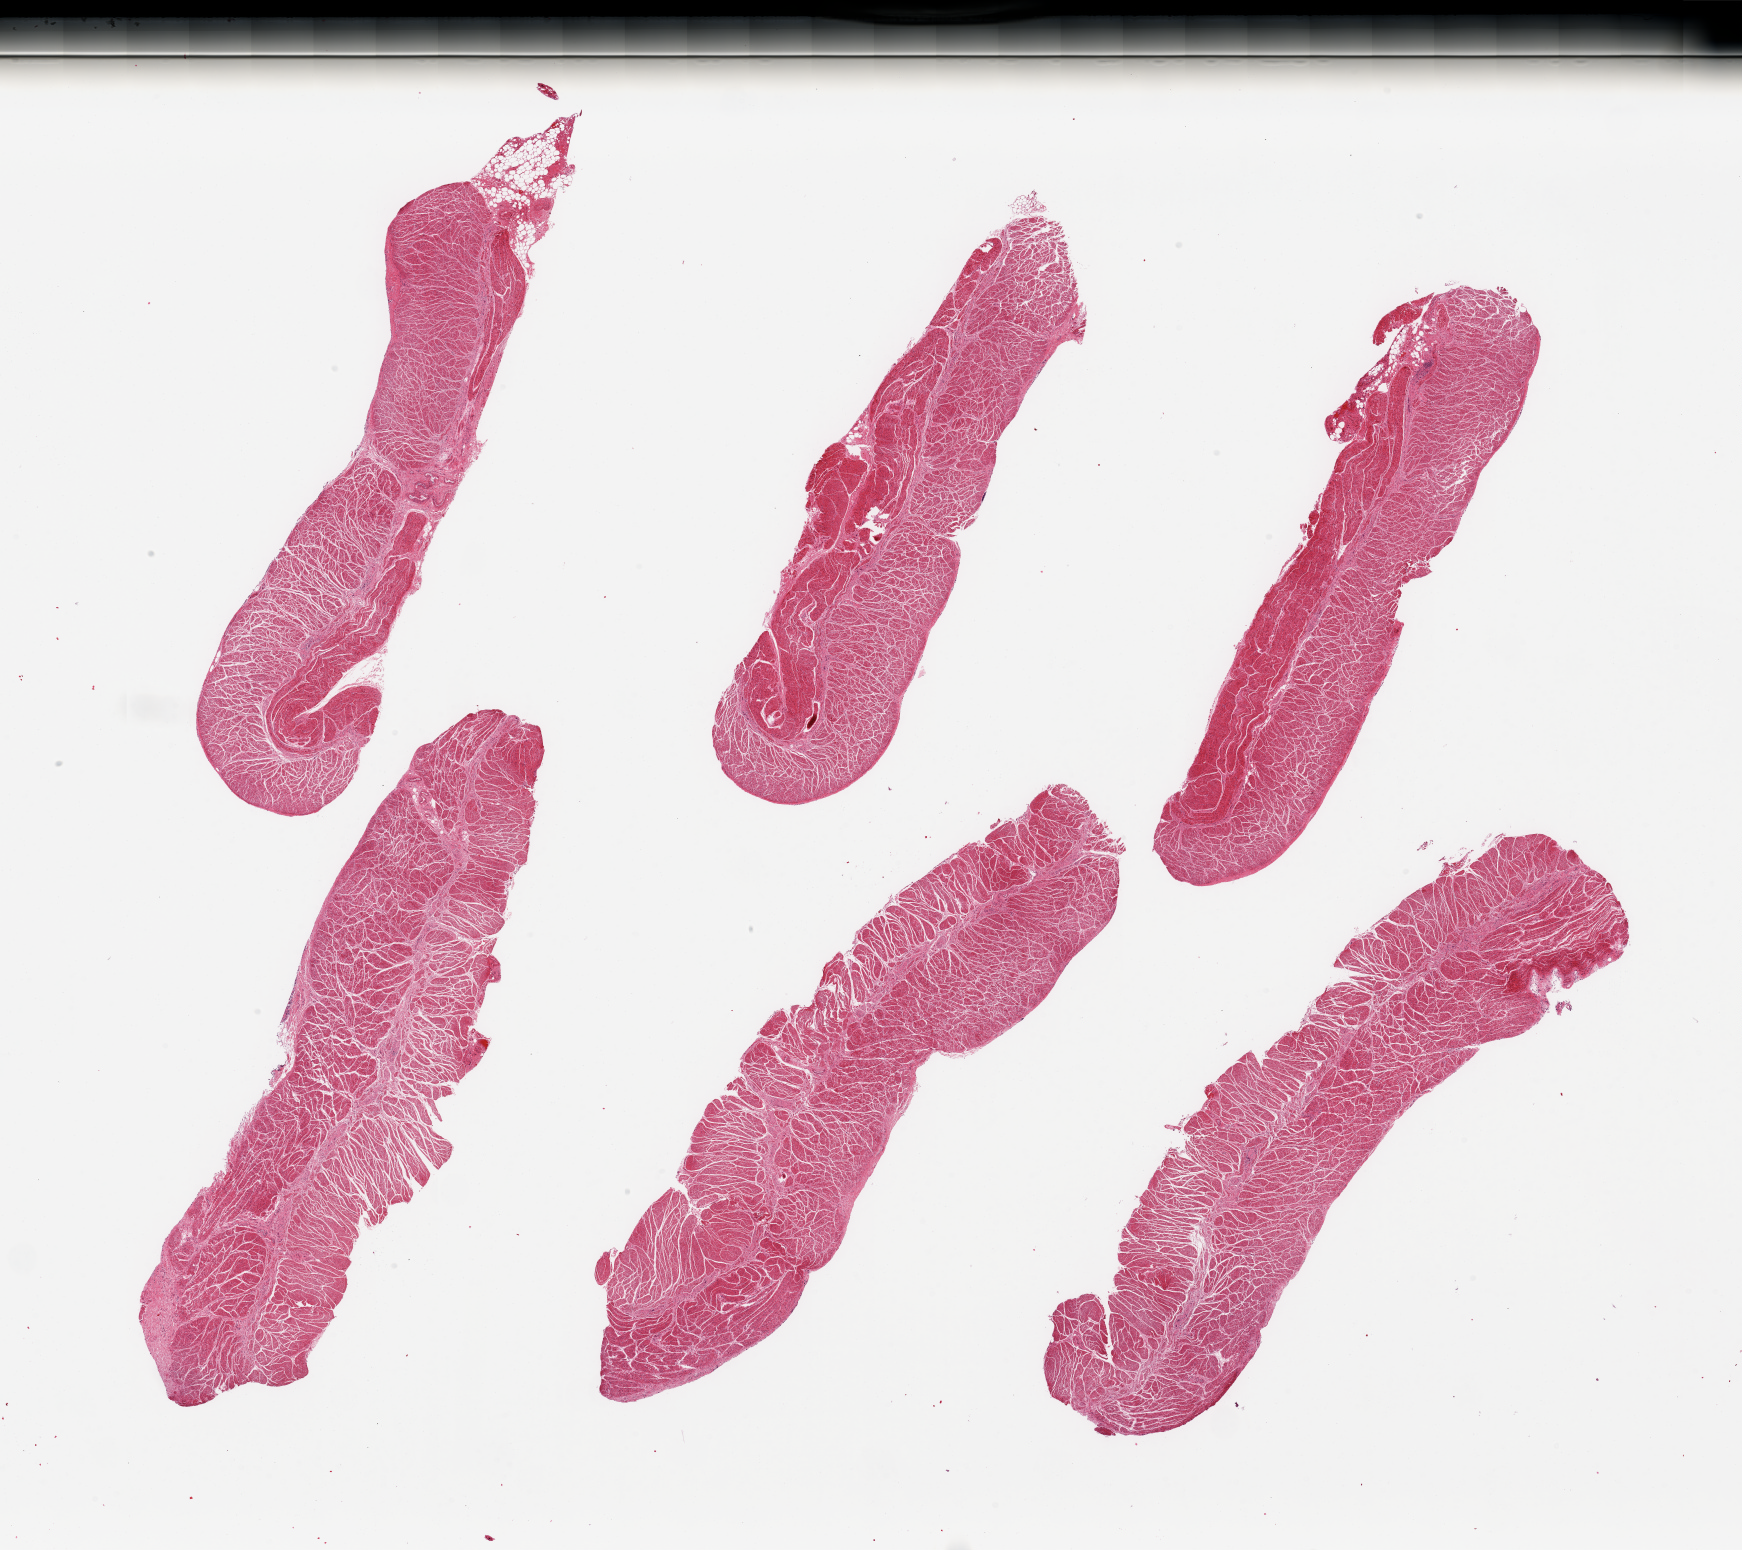
Whole-slide image, haematoxylin and eosin stain — whole scanned area (about 27.6 x 24.5 mm) shown as a low-resolution overview. PAXgene-fixed paraffin-embedded (PFPE) section. Sampled site (target tissue): esophageal muscle. Tissue donor sample. Donor: male.
Review note (as recorded): 6 pieces, confirmed target muscularis.